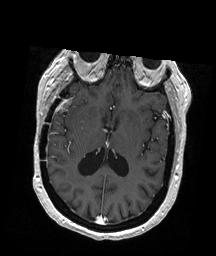
Brain MRI from a brain-tumour surgery series, one axial slice. Position 95 of 192 along the scan axis. T1-weighted post-contrast. 1 mm slice thickness. 216 × 256 image matrix. Case-level facts recorded for this patient, not image findings: histopathology: Glioblastoma; WHO grade: 4; IDH mutation: no.
Outlined on this slice (outlined manually by an expert reader):
- tumour: box from (x=58, y=97) to (x=73, y=112) px